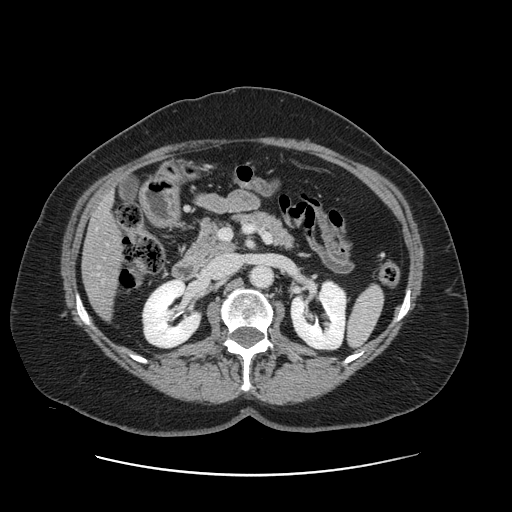
Contrast-enhanced abdominal CT, one axial slice; position 59 of 161 along the scan axis; 120 kVp; soft-tissue window (W 400 / L 40 HU); 2.5 mm slice thickness; 512 × 512 image matrix, field of view 398 × 398 mm. Female patient, age 62 years. From the clinical record (not read from this slice): diagnosis: colorectal cancer liver metastases, imaged before liver resection; multiple liver metastases: no; largest metastasis: 2.5 cm; disease in both lobes: no.
Outlined on this slice (expert manual segmentation):
- liver: bounding box <83,196,121,316> (left, top, right, bottom; pixels)